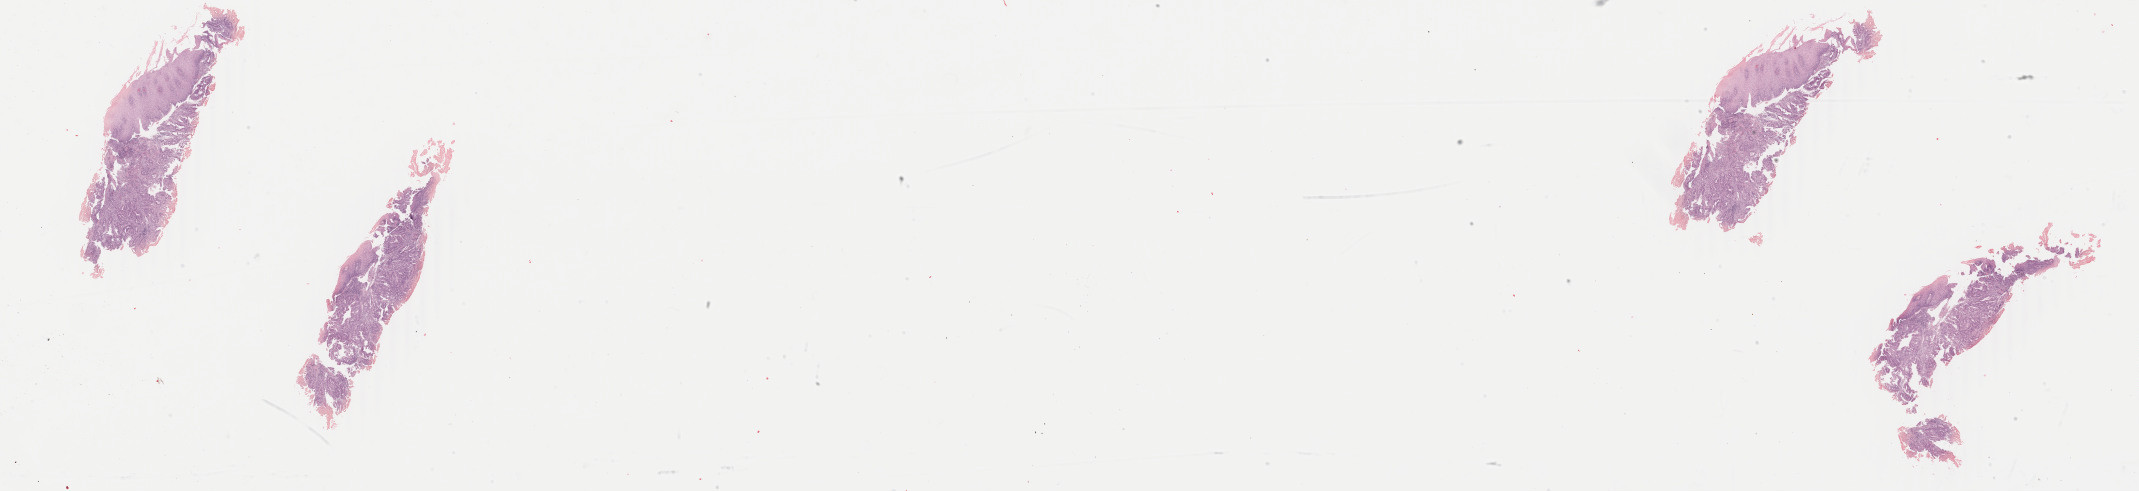
Digitized H&E-stained tissue section (whole slide), low-resolution overview of the scanned area, about 34.0 x 7.8 mm, formalin-fixed paraffin-embedded (FFPE) diagnostic section, primary tumour sample from the stomach. Patient: male, age at initial diagnosis 71 years. Histologic grade: G3 (poorly differentiated). Slide review estimates, as recorded: tumour cells 70%, tumour nuclei 70%, normal cells 8%, stromal cells 21%, necrosis 1%. Infiltration values recorded for this section: lymphocyte infiltration 2%, monocyte infiltration 1%, neutrophil infiltration 5%.
Diagnosis: Adenocarcinoma, intestinal type (cardia, NOS). AJCC pathologic stage: IIIB (6th edition).